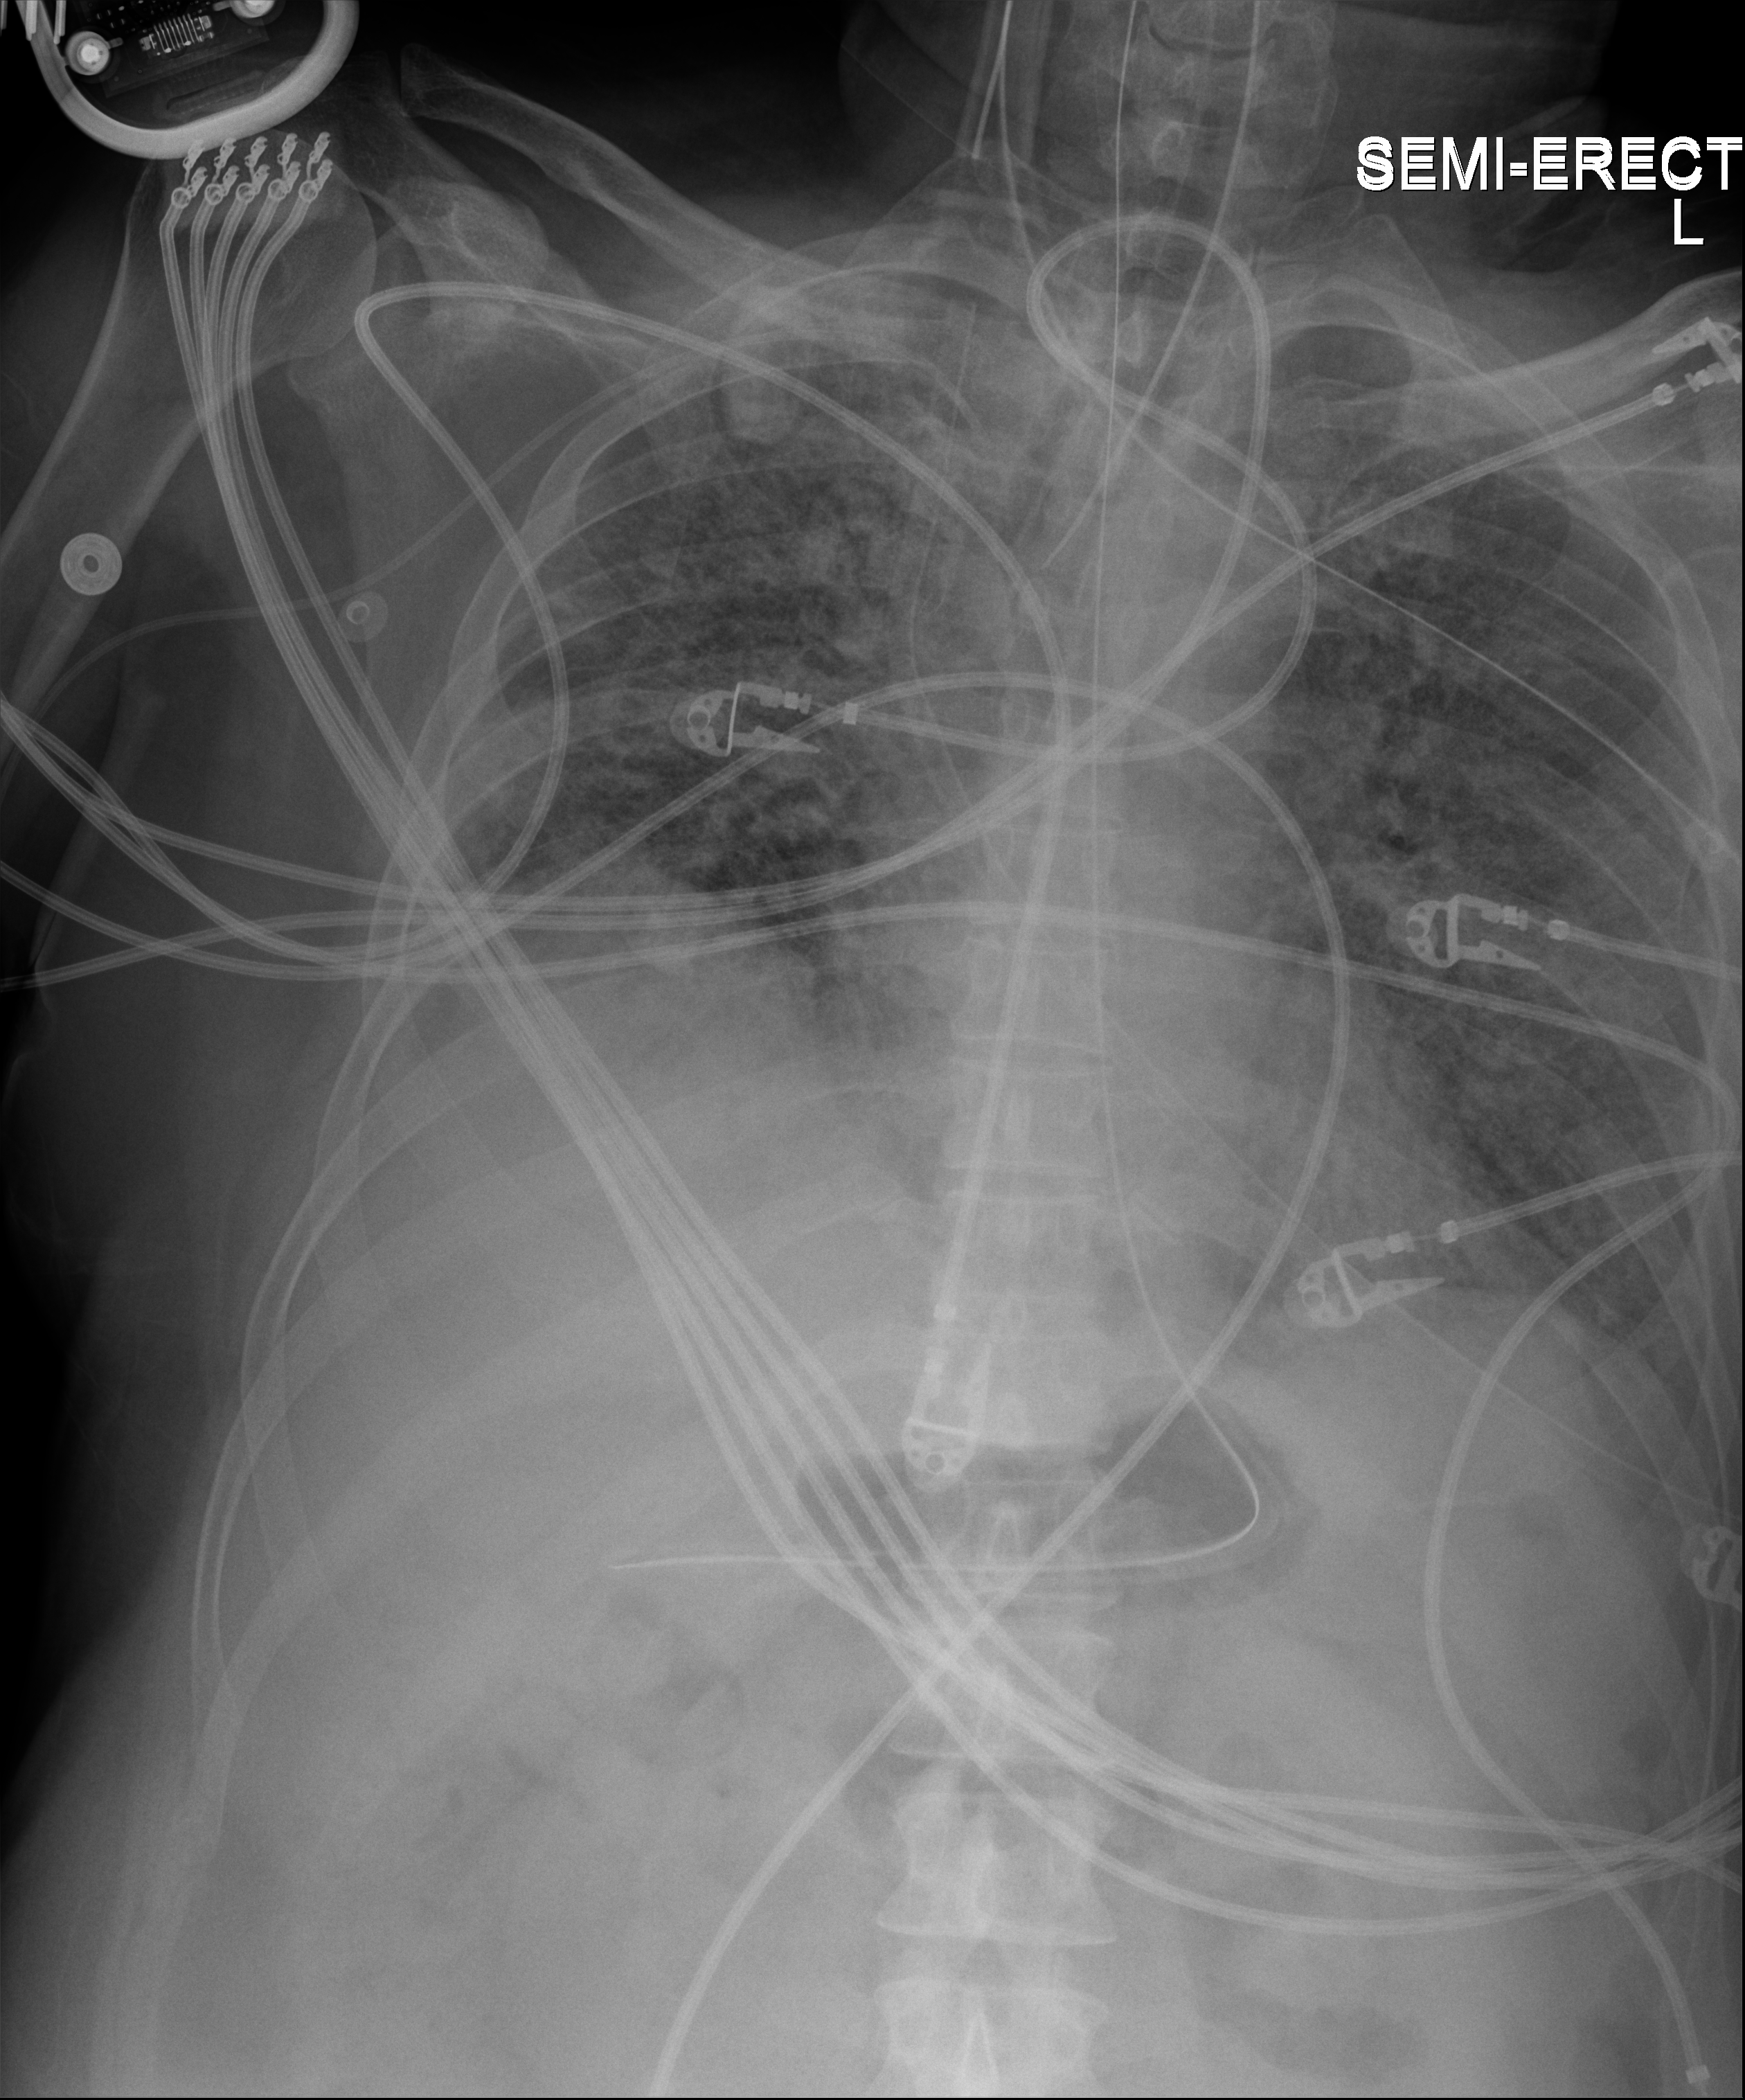
Chest X-ray (portable), anteroposterior (AP) projection. Male patient hospitalised with COVID-19, age 18–59 years.
From the hospital-stay record, not from the radiograph (when in the stay this image was taken is not recorded):
- smoking status (admission record): never
- hypertension (admission record): no
- mechanically ventilated during this hospital stay: yes